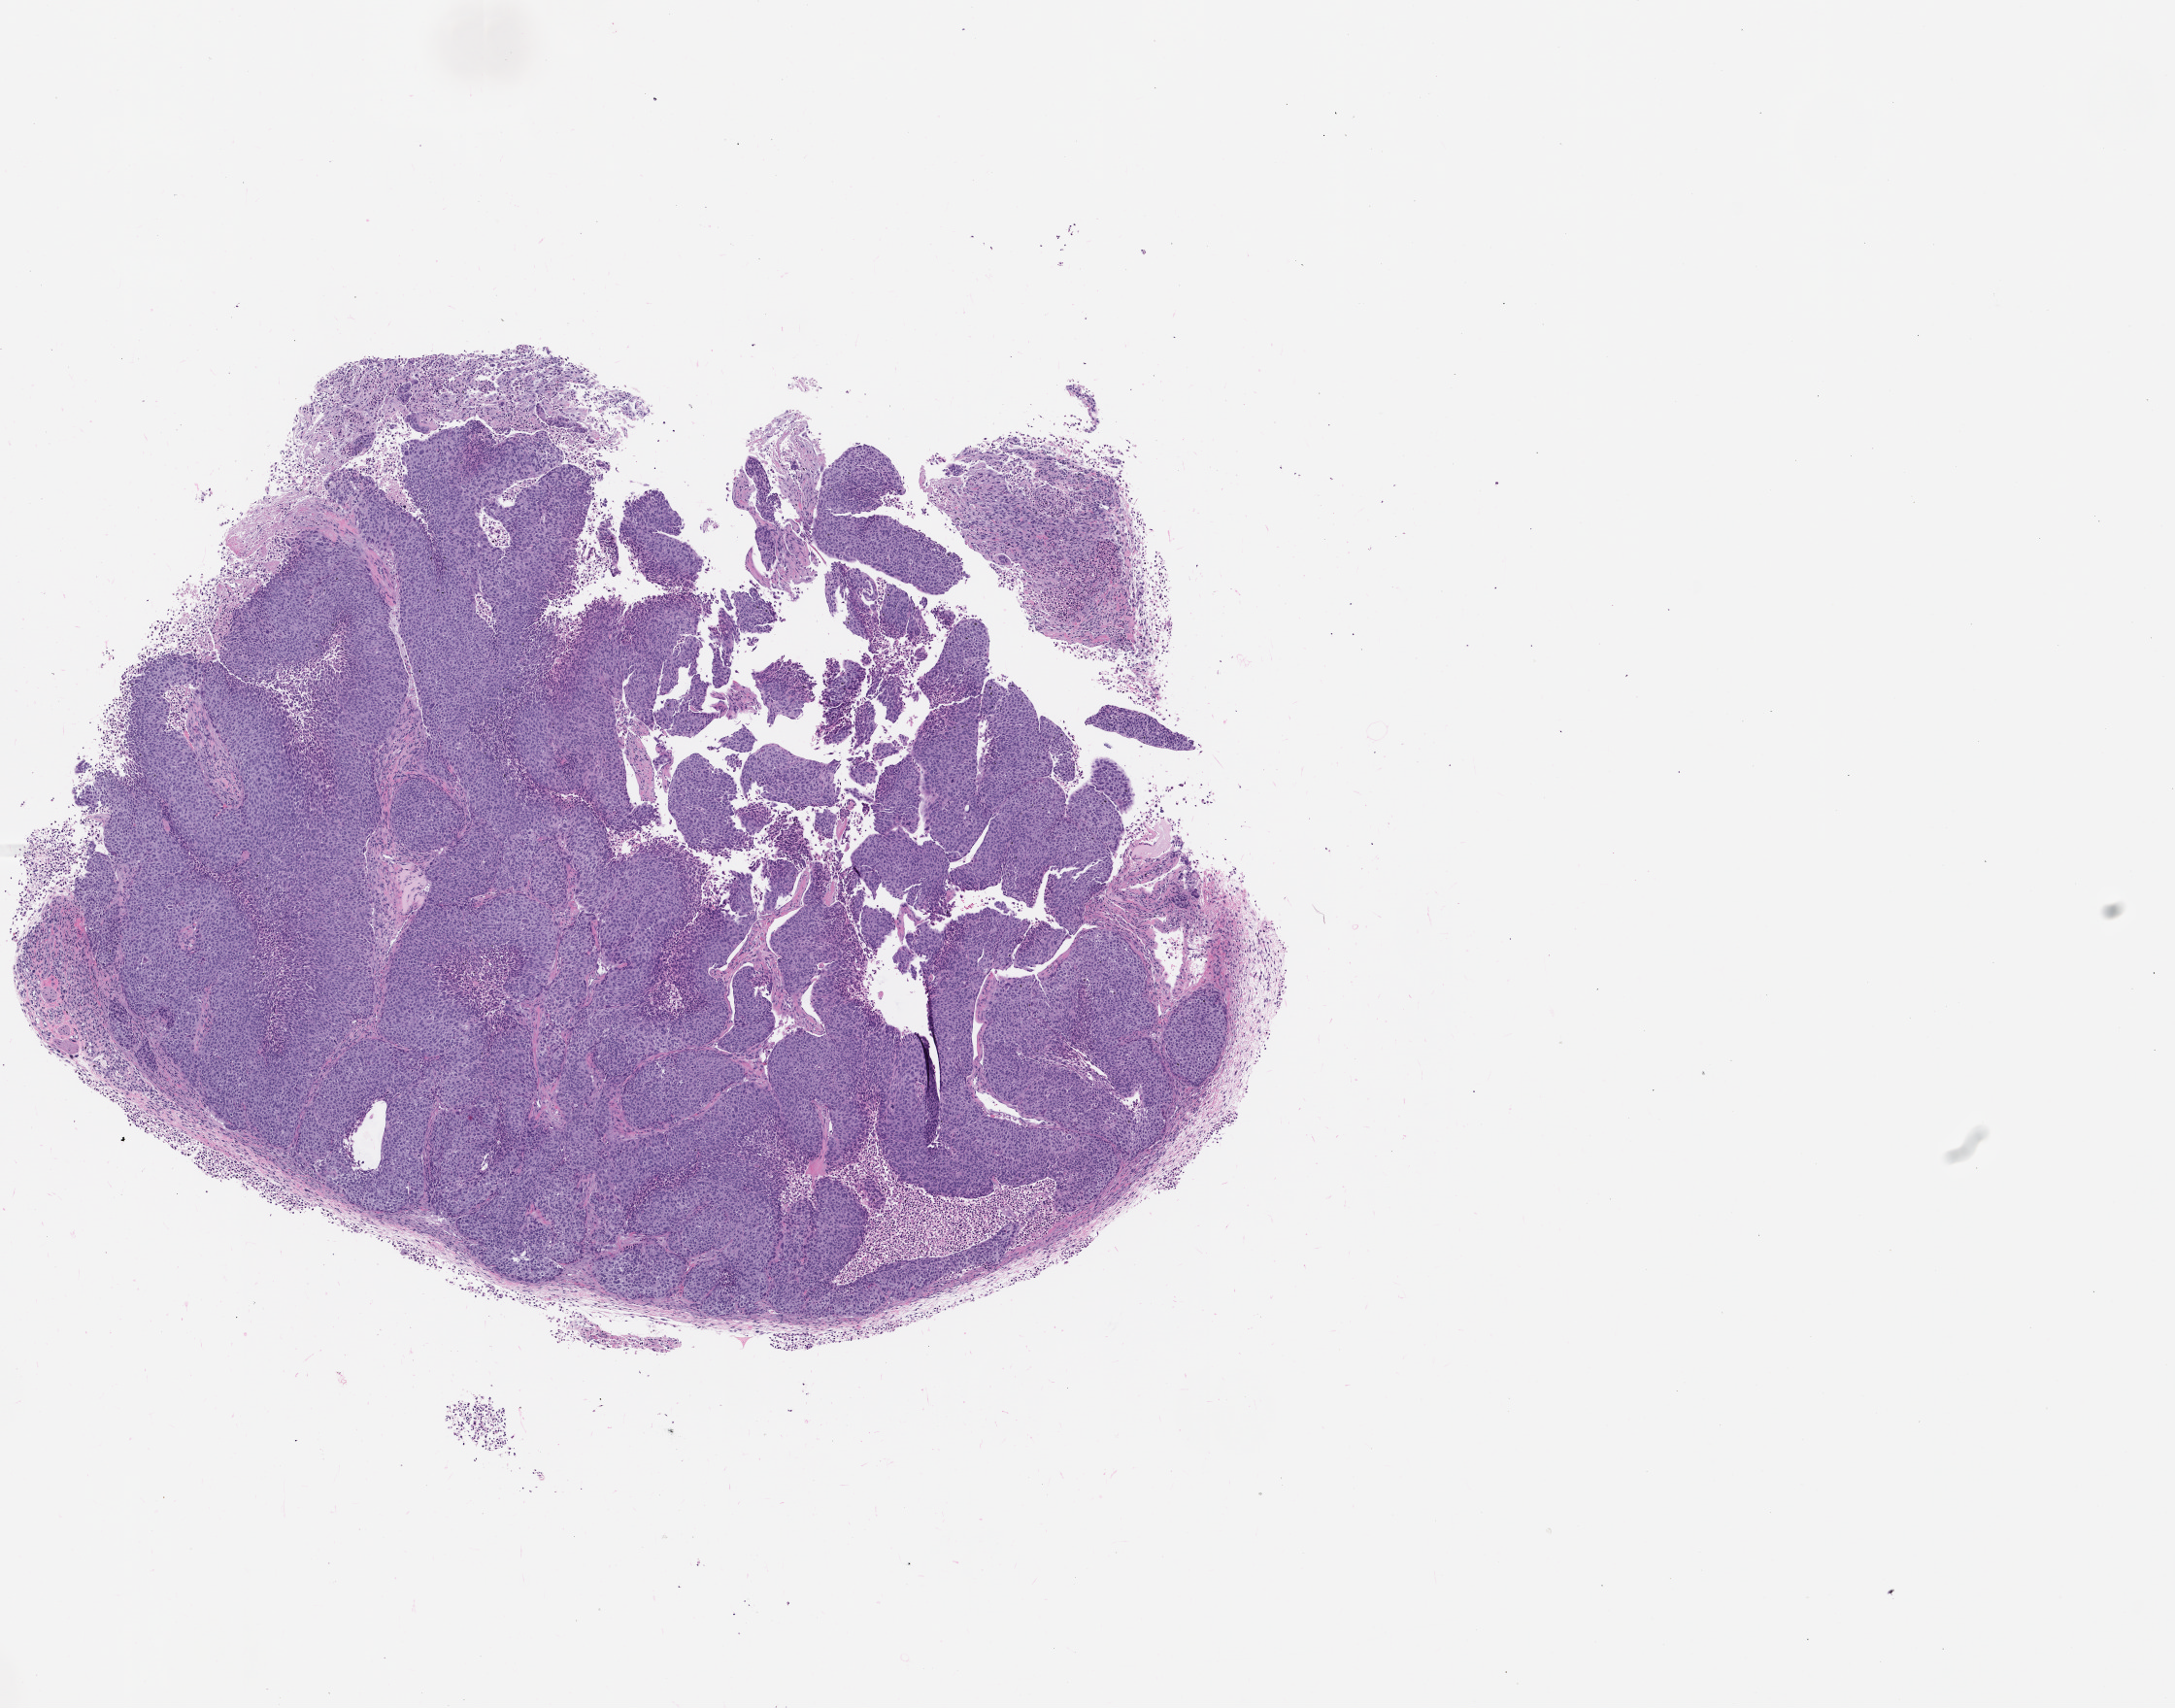
Whole-slide image, hematoxylin and eosin (H&E): patient-derived xenograft (human tumor grown in a mouse), passage 1 — shown as a low-resolution overview of the whole scanned area (about 9.0 x 7.0 mm), FFPE section, originating tumor site category: head and neck.
* originating patient diagnosis: Head and Neck Squamous Cell Carcinoma